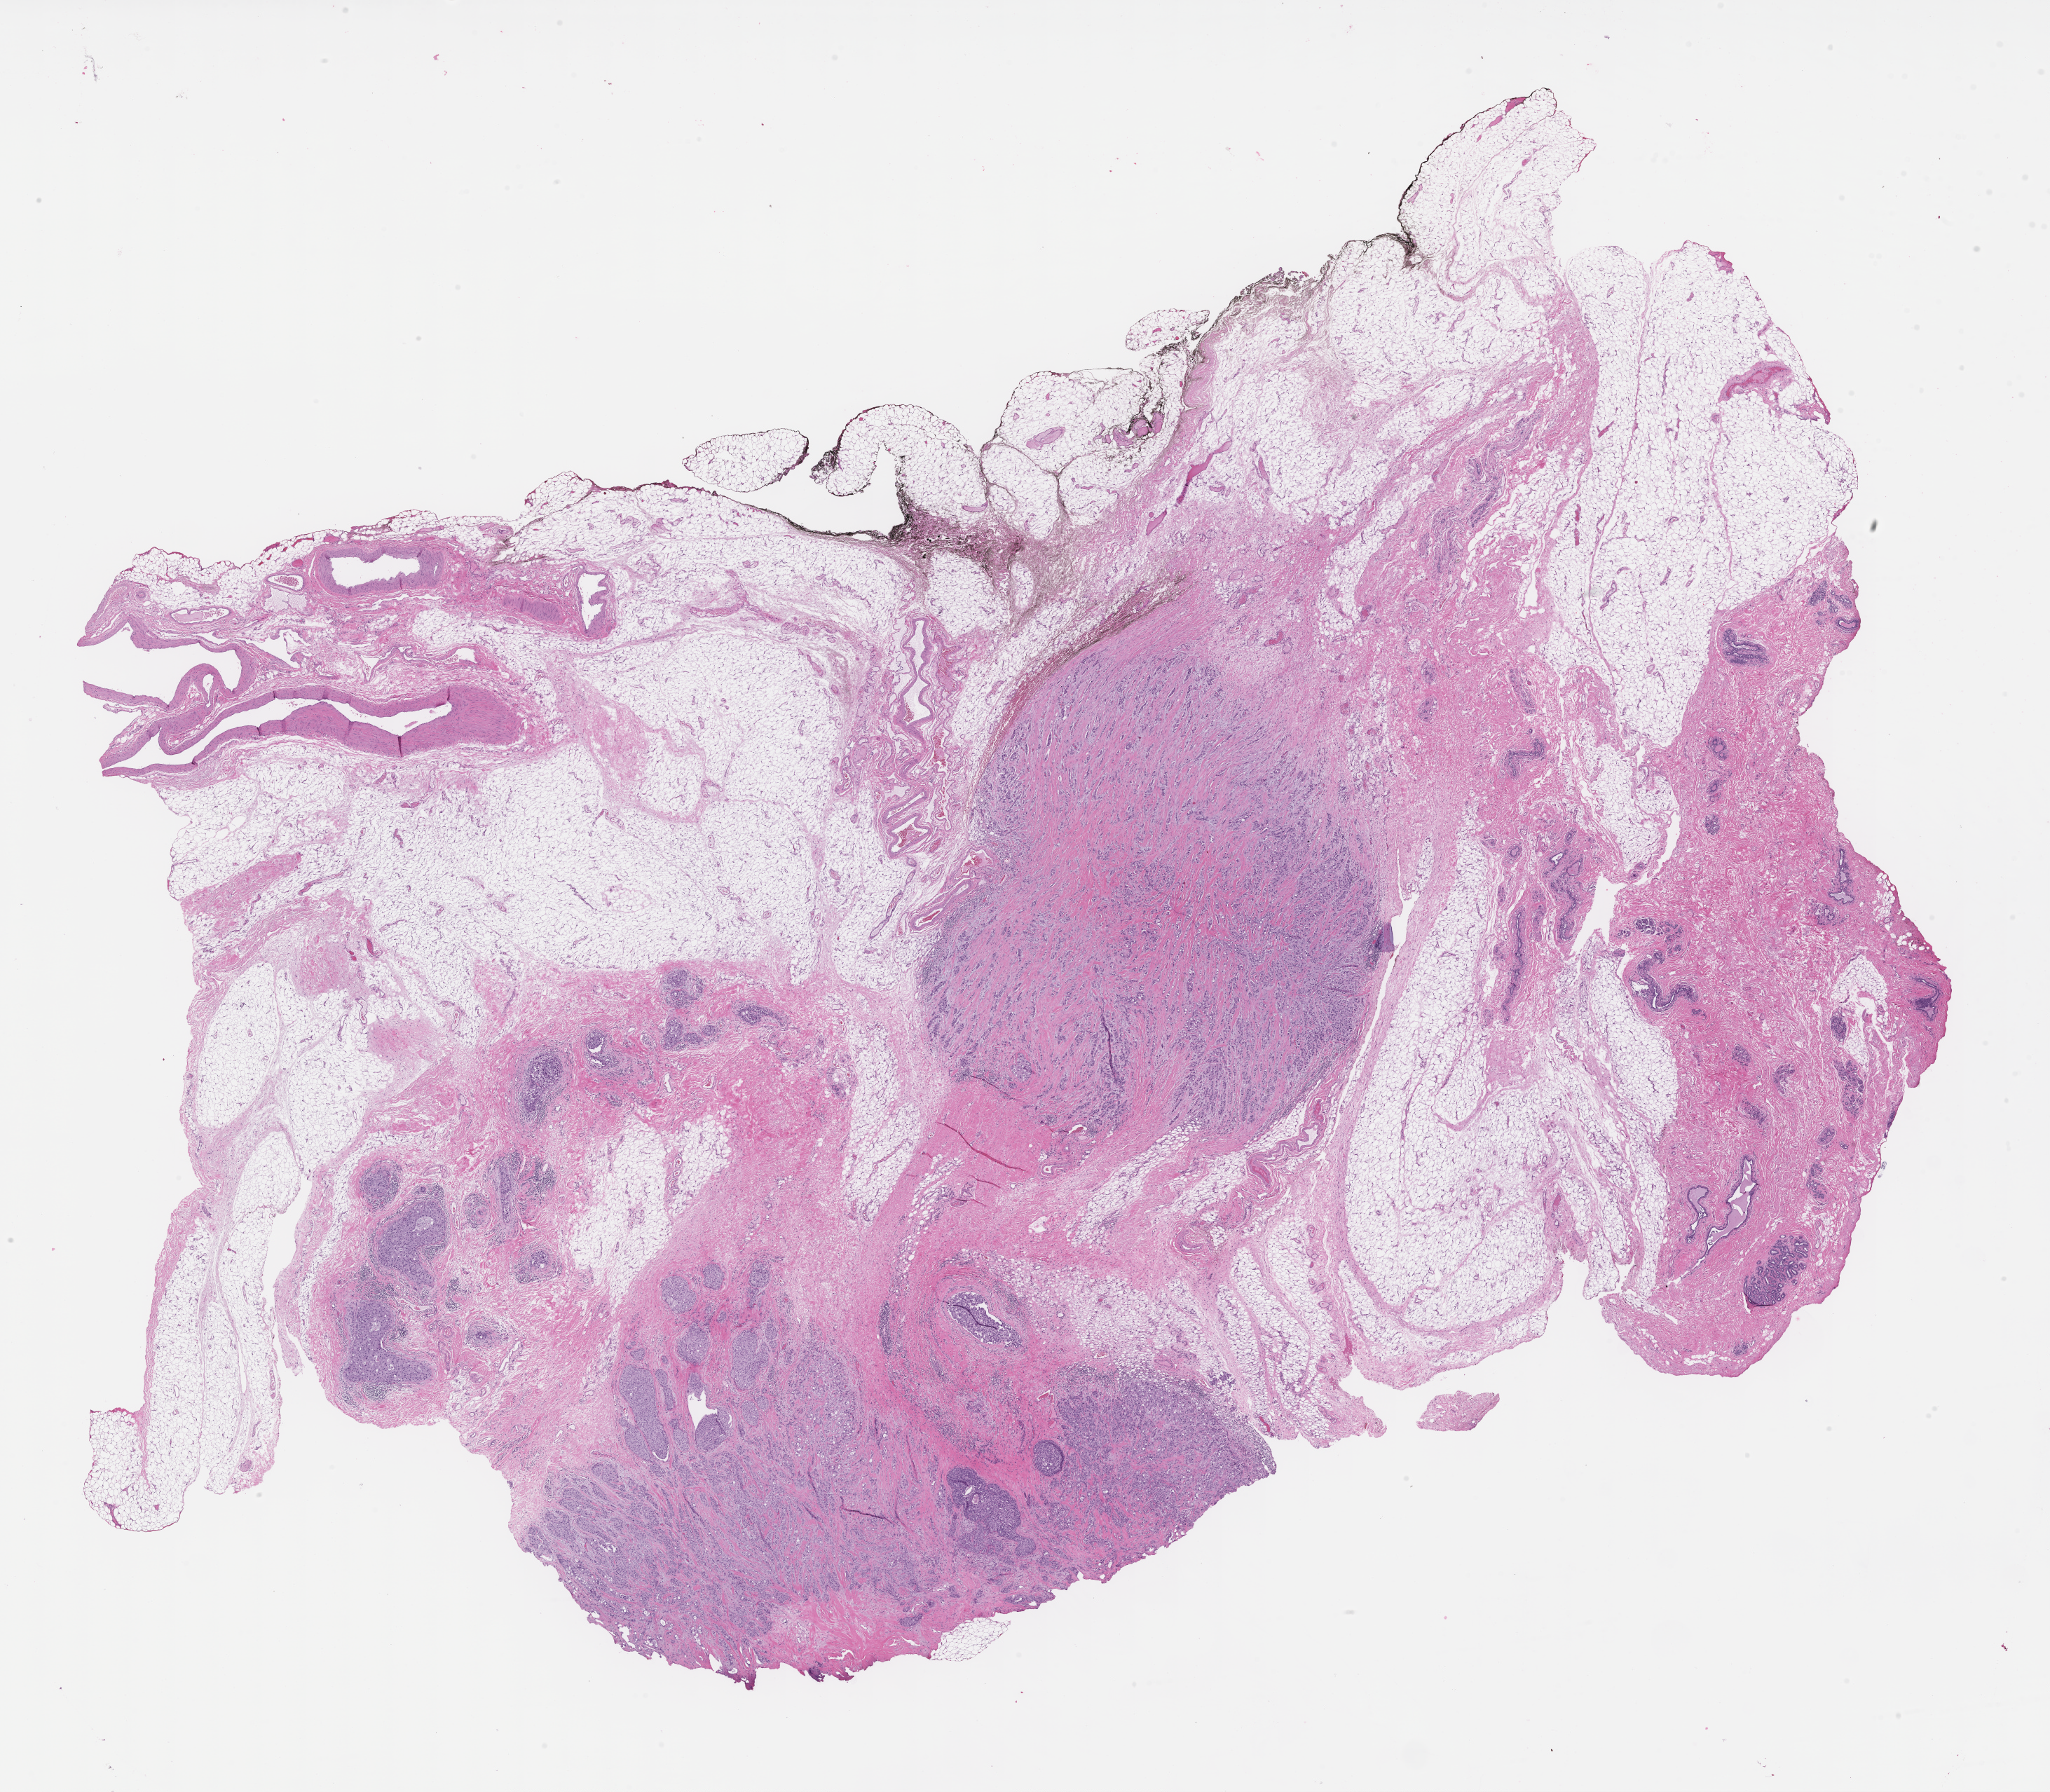
Digitized hematoxylin and eosin (H&E)-stained section — whole scanned area (about 23.6 x 20.6 mm) shown as a low-resolution overview; formalin-fixed paraffin-embedded section; tissue site: breast; specimen time point: archival tissue. Patient: female.
This section: primary tumour tissue. Diagnosis: Invasive Breast Carcinoma.